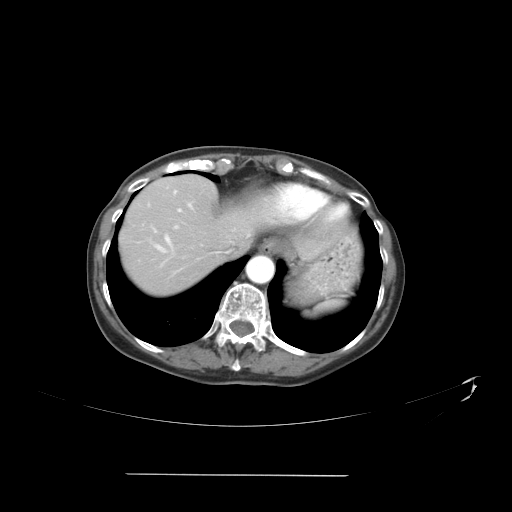
Contrast-enhanced abdominal CT, one axial slice; position 33 of 41 along the scan axis; intravenous contrast given; soft-tissue window (W 400 / L 40 HU); 5 mm slice thickness; 512 × 512 image matrix, field of view 431 × 431 mm. Female patient, age 74 years. From the clinical record (not read from this slice): diagnosis: colorectal cancer liver metastases, imaged before liver resection; multiple liver metastases: yes; largest metastasis: 3.3 cm; disease in both lobes: yes.
Outlined on this slice (outlined manually by an expert reader):
- hepatic veins: bounding box (x1, y1, x2, y2) in pixels: (154, 199, 275, 268)
- liver: (121, 175, 255, 293)
- planned liver remnant (the part of the liver to remain after resection): (123, 175, 255, 255)
- portal vein (with intrahepatic branches): (165, 209, 181, 245)